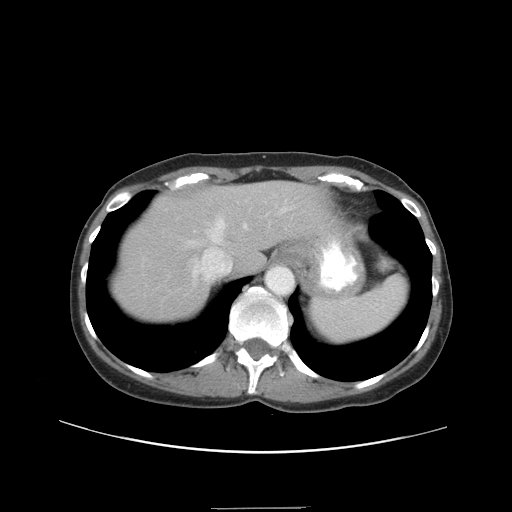
Contrast-enhanced abdominal CT, one axial slice. Position 31 of 38 along the scan axis. Reconstruction kernel STANDARD. Intravenous contrast given. Soft-tissue window (W 400 / L 40 HU). 512 × 512 image matrix, field of view 388 × 388 mm. Female patient, age 64 years. Case-level facts recorded for this patient, not image findings: diagnosis: colorectal cancer liver metastases, imaged before liver resection; multiple liver metastases: no; largest metastasis: 3.8 cm.
Annotated regions visible in this slice (outlined manually by an expert reader):
- hepatic veins: bounding box [x1, y1, x2, y2] px = [188, 207, 291, 280]
- liver: [113, 183, 321, 321]
- planned liver remnant (the part of the liver to remain after resection): [154, 183, 322, 270]